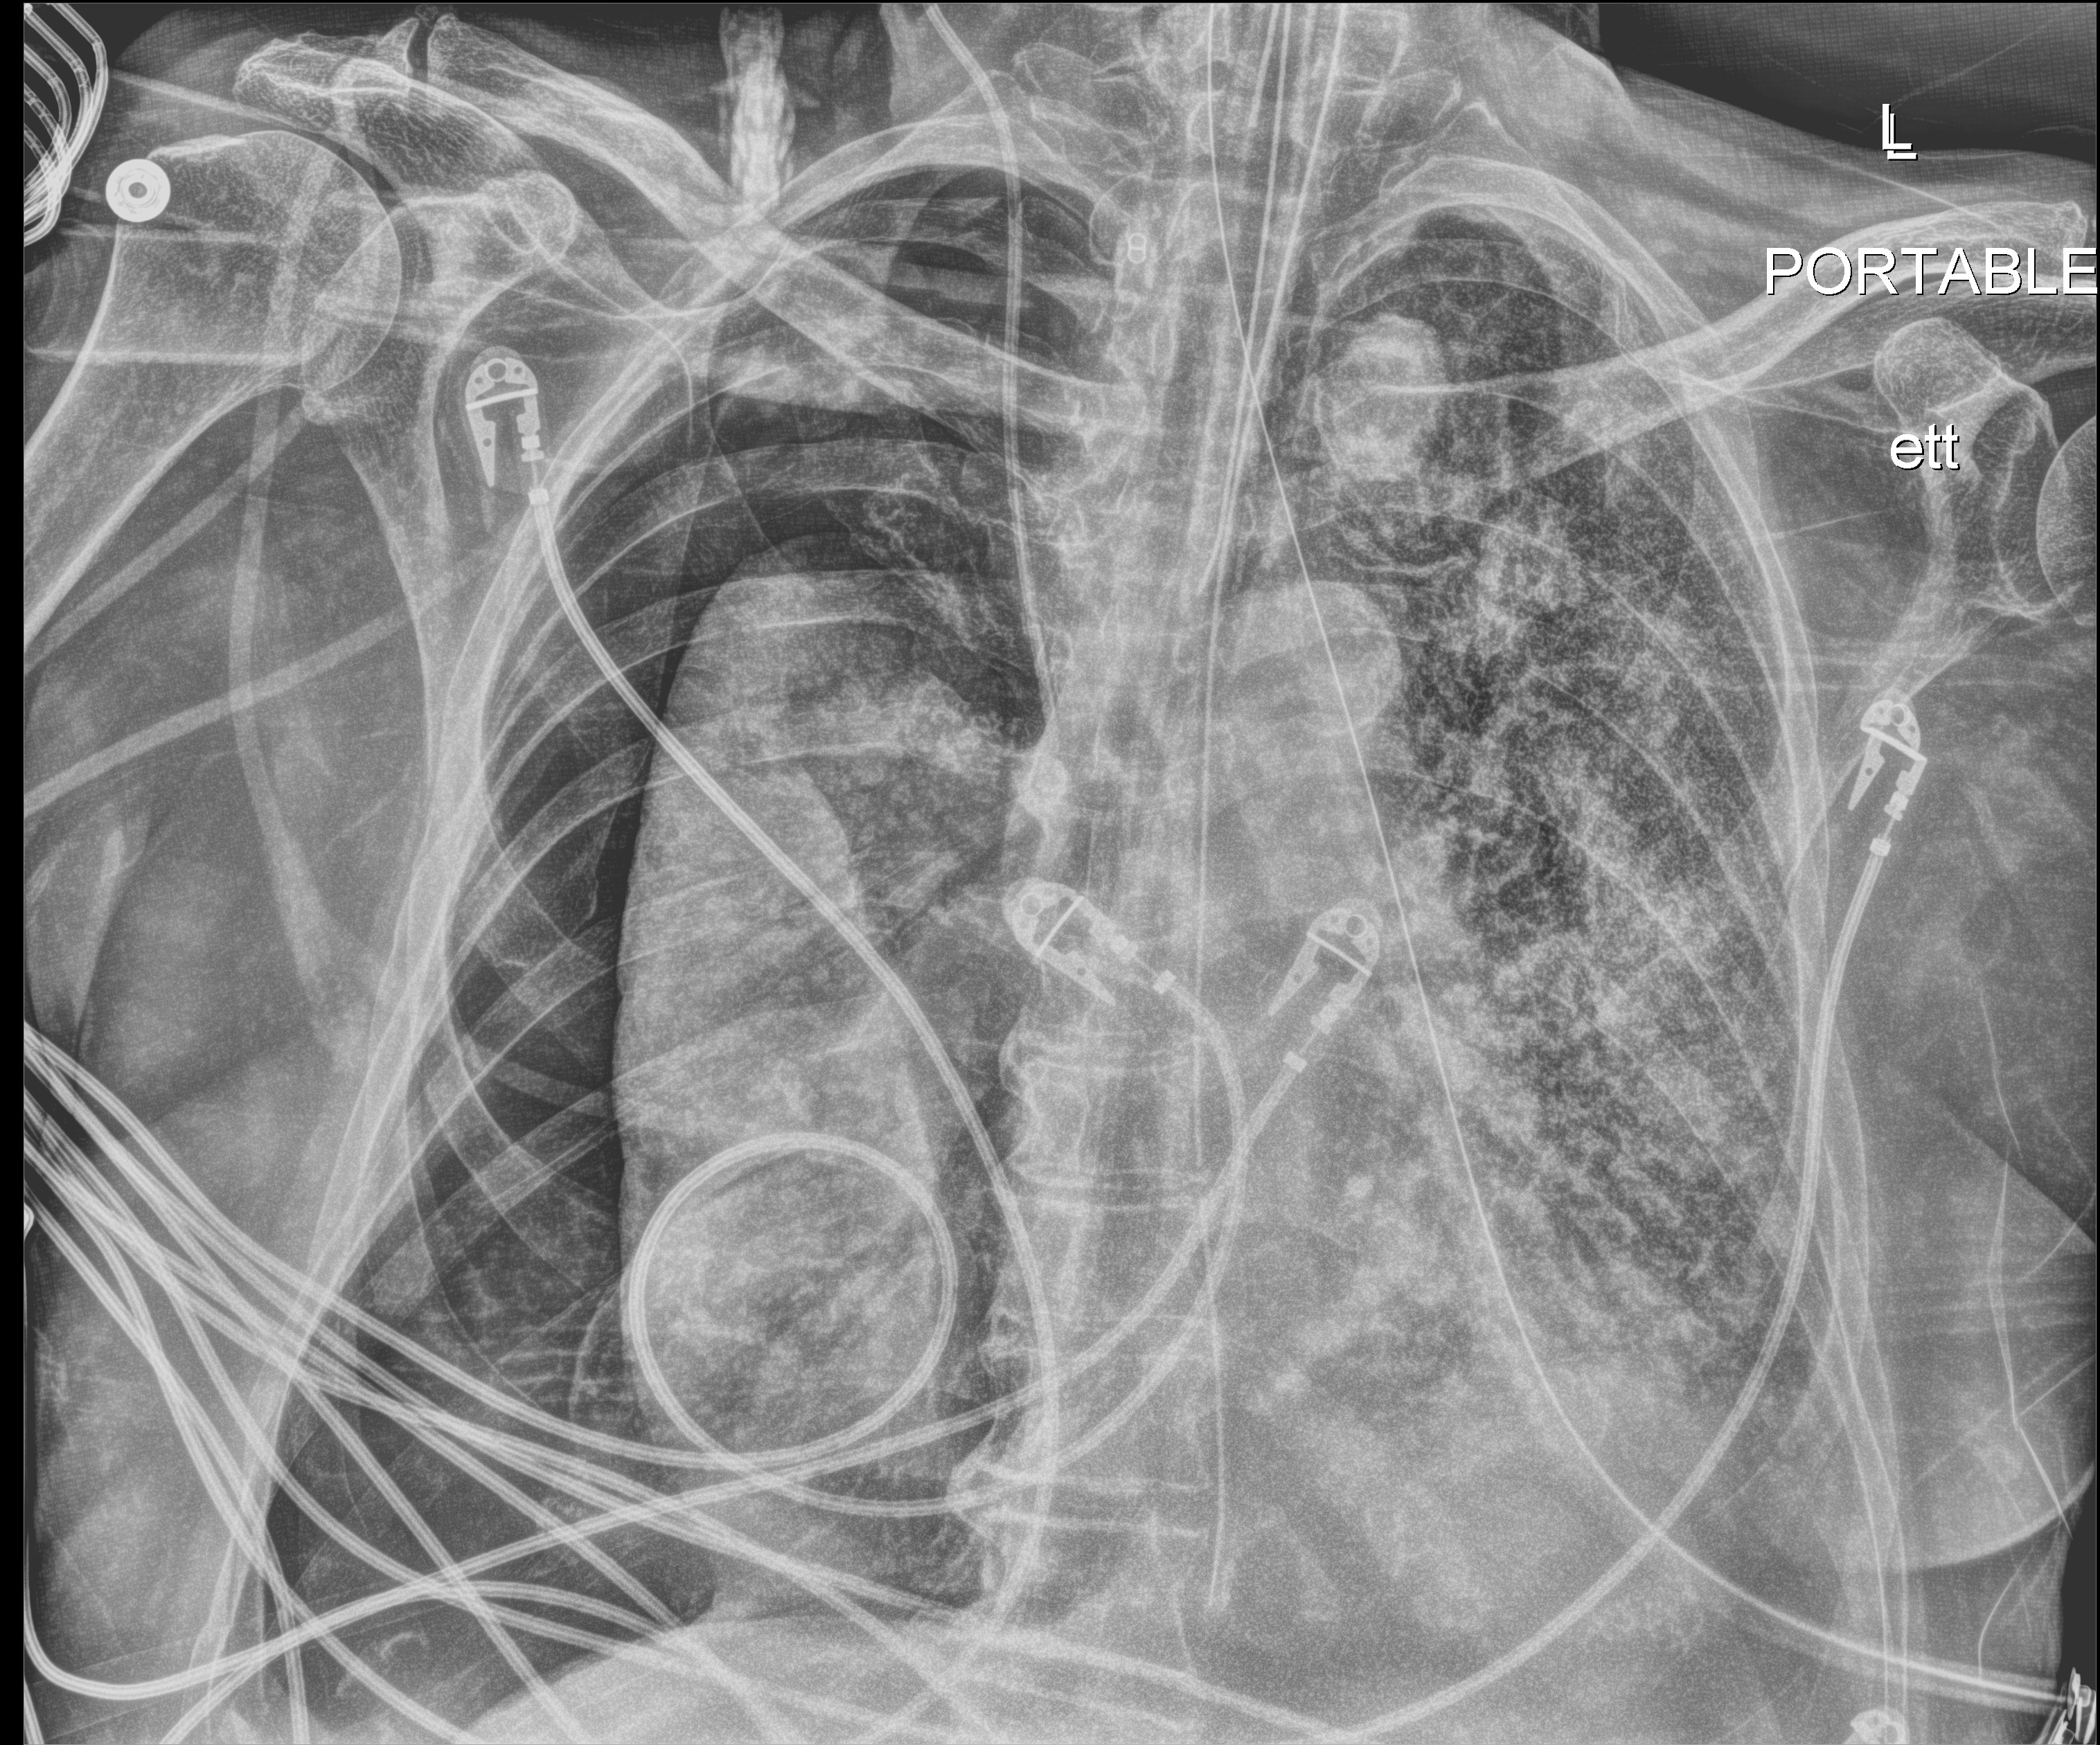
Bedside chest radiograph (digital radiography), anteroposterior (AP) projection. Patient hospitalised with COVID-19; male, aged 75–90 years.
Admission-level facts for this patient (not findings on this image; timing relative to this image not recorded): mechanically ventilated during this hospital stay: yes.